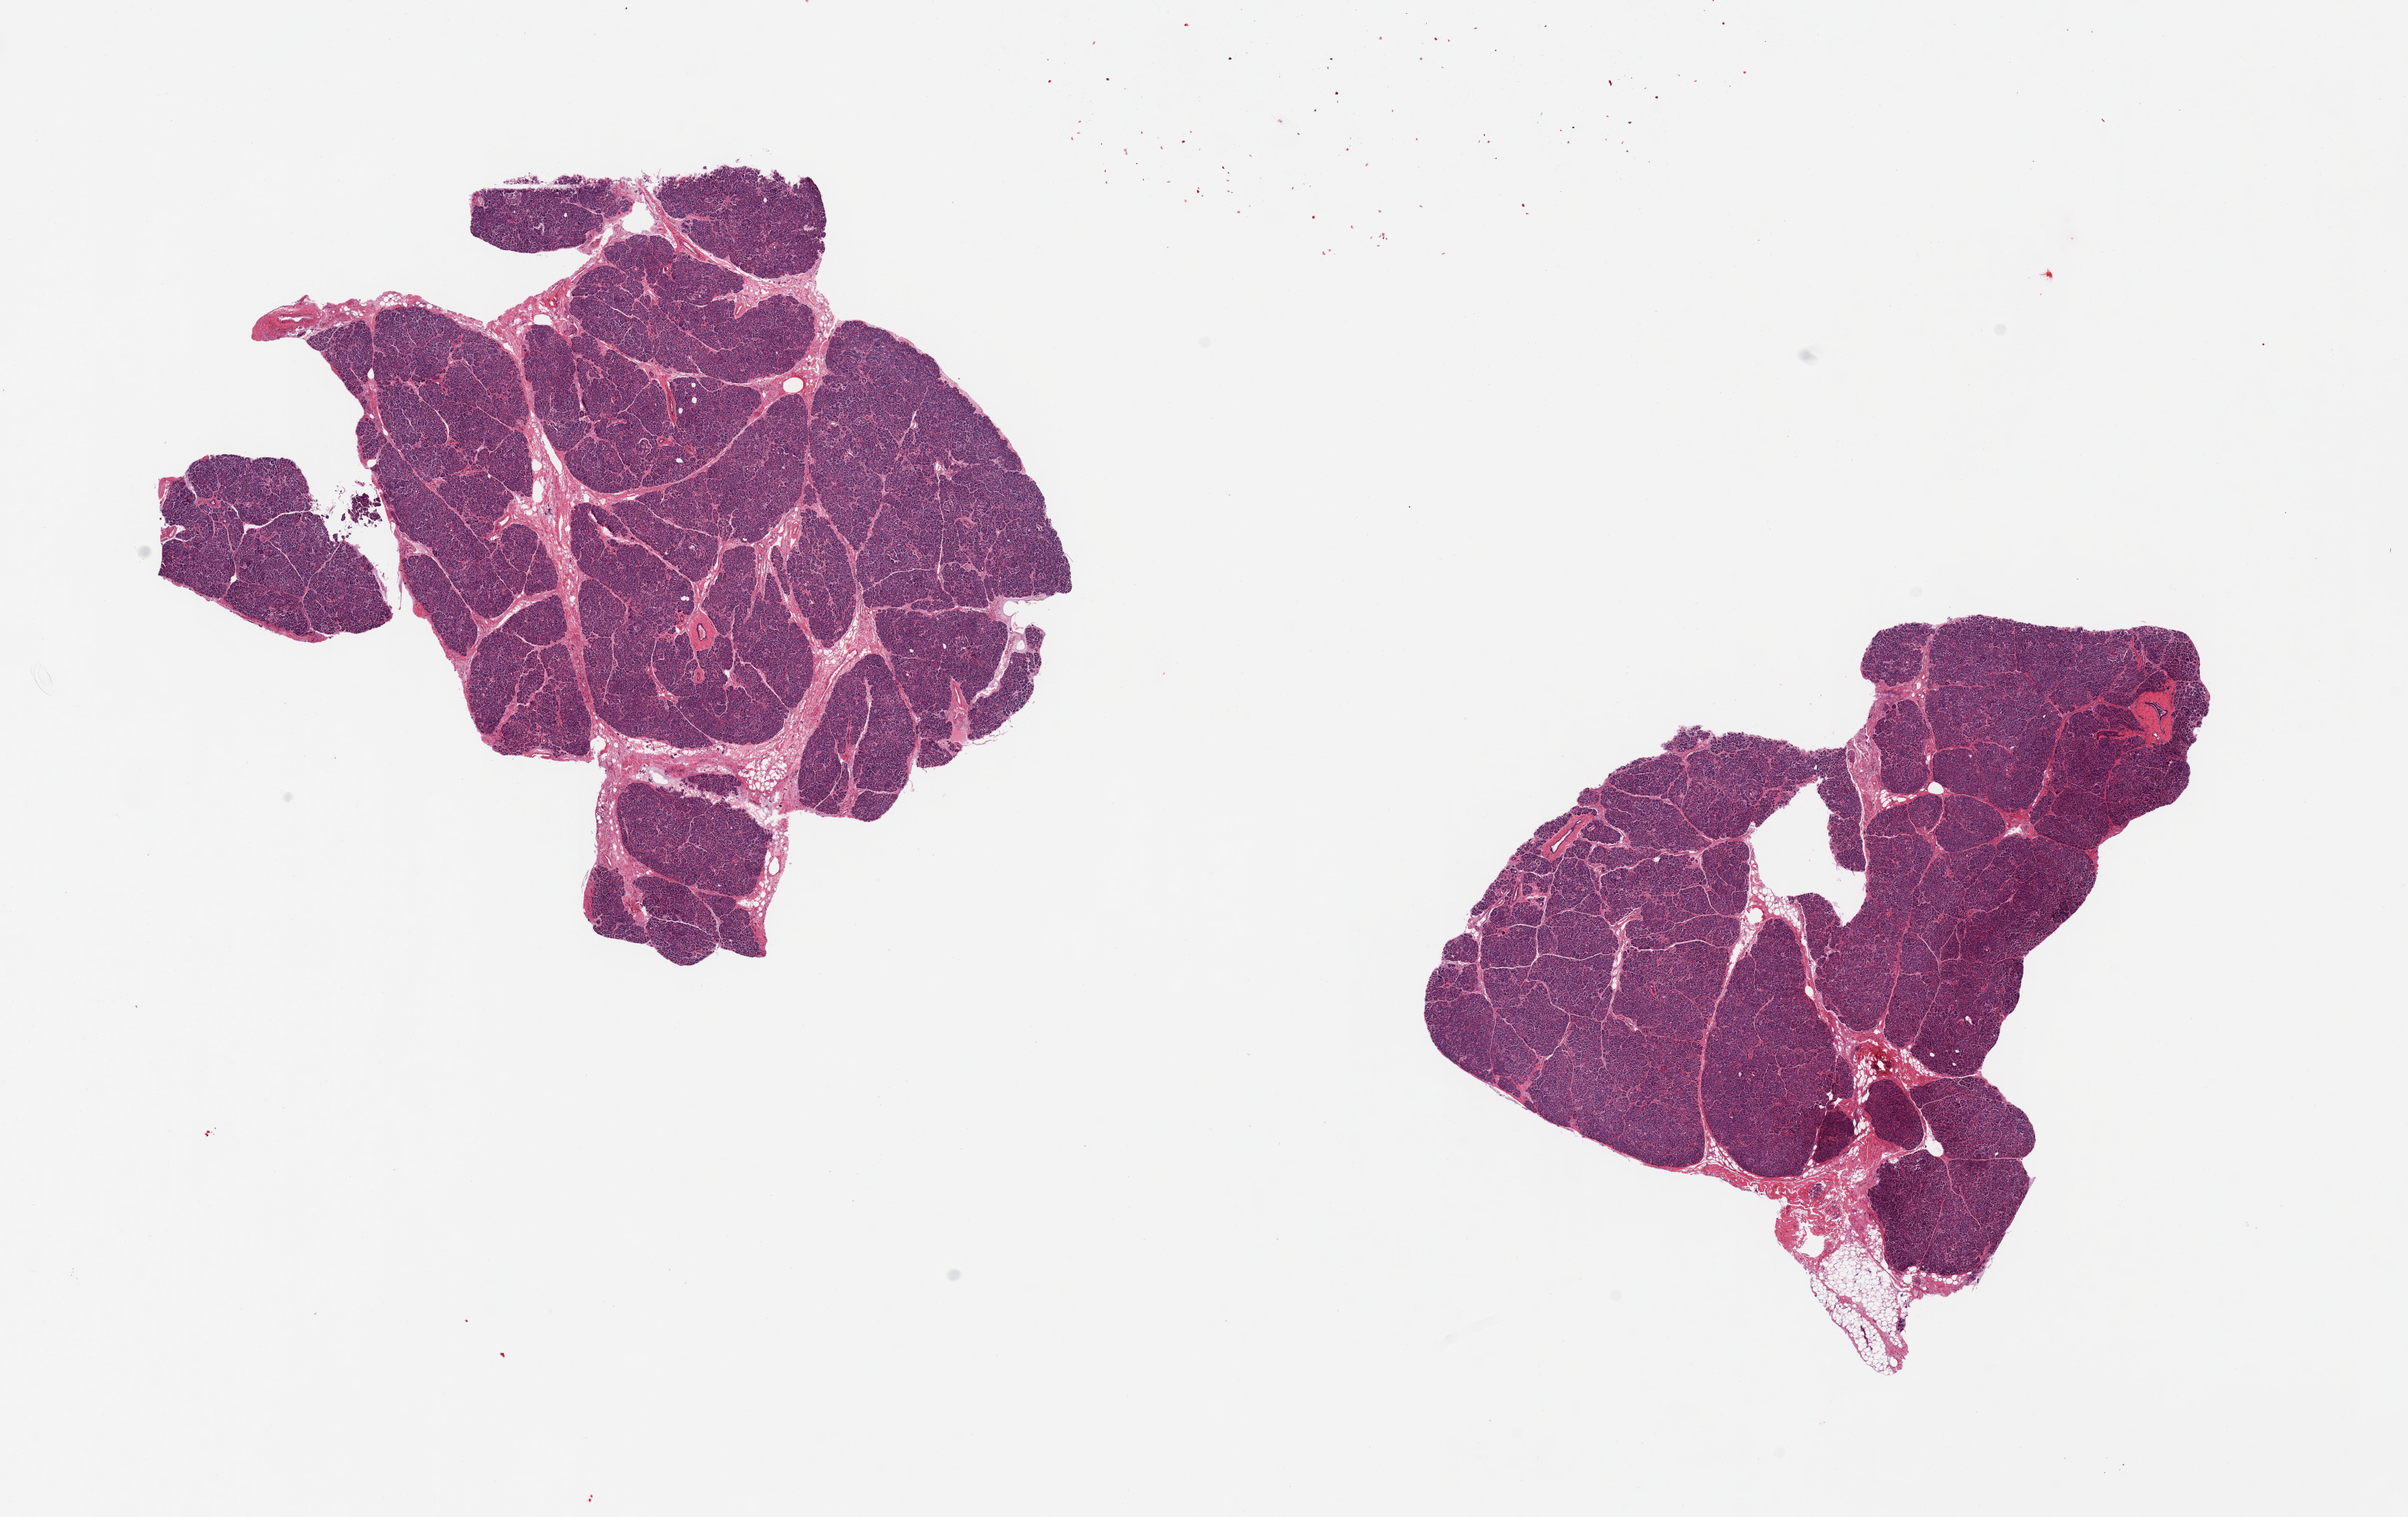
Digitized hematoxylin and eosin (H&E)-stained section, brightfield — shown as a low-resolution overview of the whole scanned area (about 24.6 x 15.5 mm); PAXgene-fixed paraffin-embedded (PFPE) section; section of pancreas (target tissue); donor tissue sample. Donor: female.
Review note (as recorded): 2 pieces; islets small and sparse.